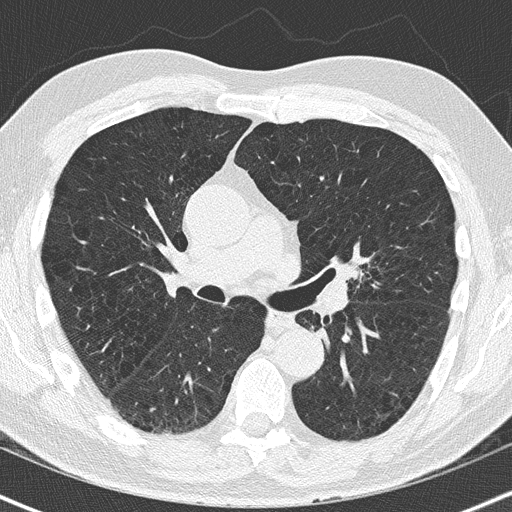
Low-dose screening chest CT, one axial slice. Slice 92 of 163 in the series (ordered by position). Reconstruction kernel B50f. Lung window (W 1500 / L -600 HU). 2 mm slice thickness. 512 × 512 image matrix, field of view 320 × 320 mm.
Annotated regions visible in this slice (manually delineated by an expert):
- lesion 1 (tumor, upper lobe of left lung): bounding box [x1, y1, x2, y2] px = [335, 265, 360, 281]